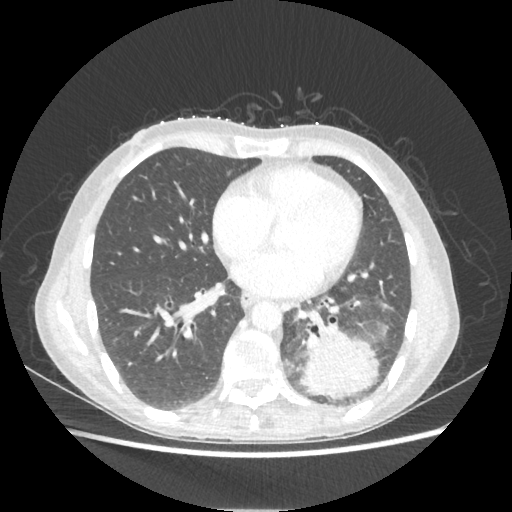
Chest CT, one axial slice. Slice 92 of 221 in the series (ordered by position). Lung window (W 1500 / L -600 HU). 1.25 mm slice thickness. 512 × 512 image matrix, field of view 360 × 360 mm. Female patient, age 53 years. From the clinical record (not read from this slice): clinical TNM (as recorded): T3 N0 M0.
Annotated regions visible in this slice (bounding box drawn by a radiologist):
- lung tumour (recorded histology: adenocarcinoma): bounding box <298,326,379,400> (left, top, right, bottom; pixels)